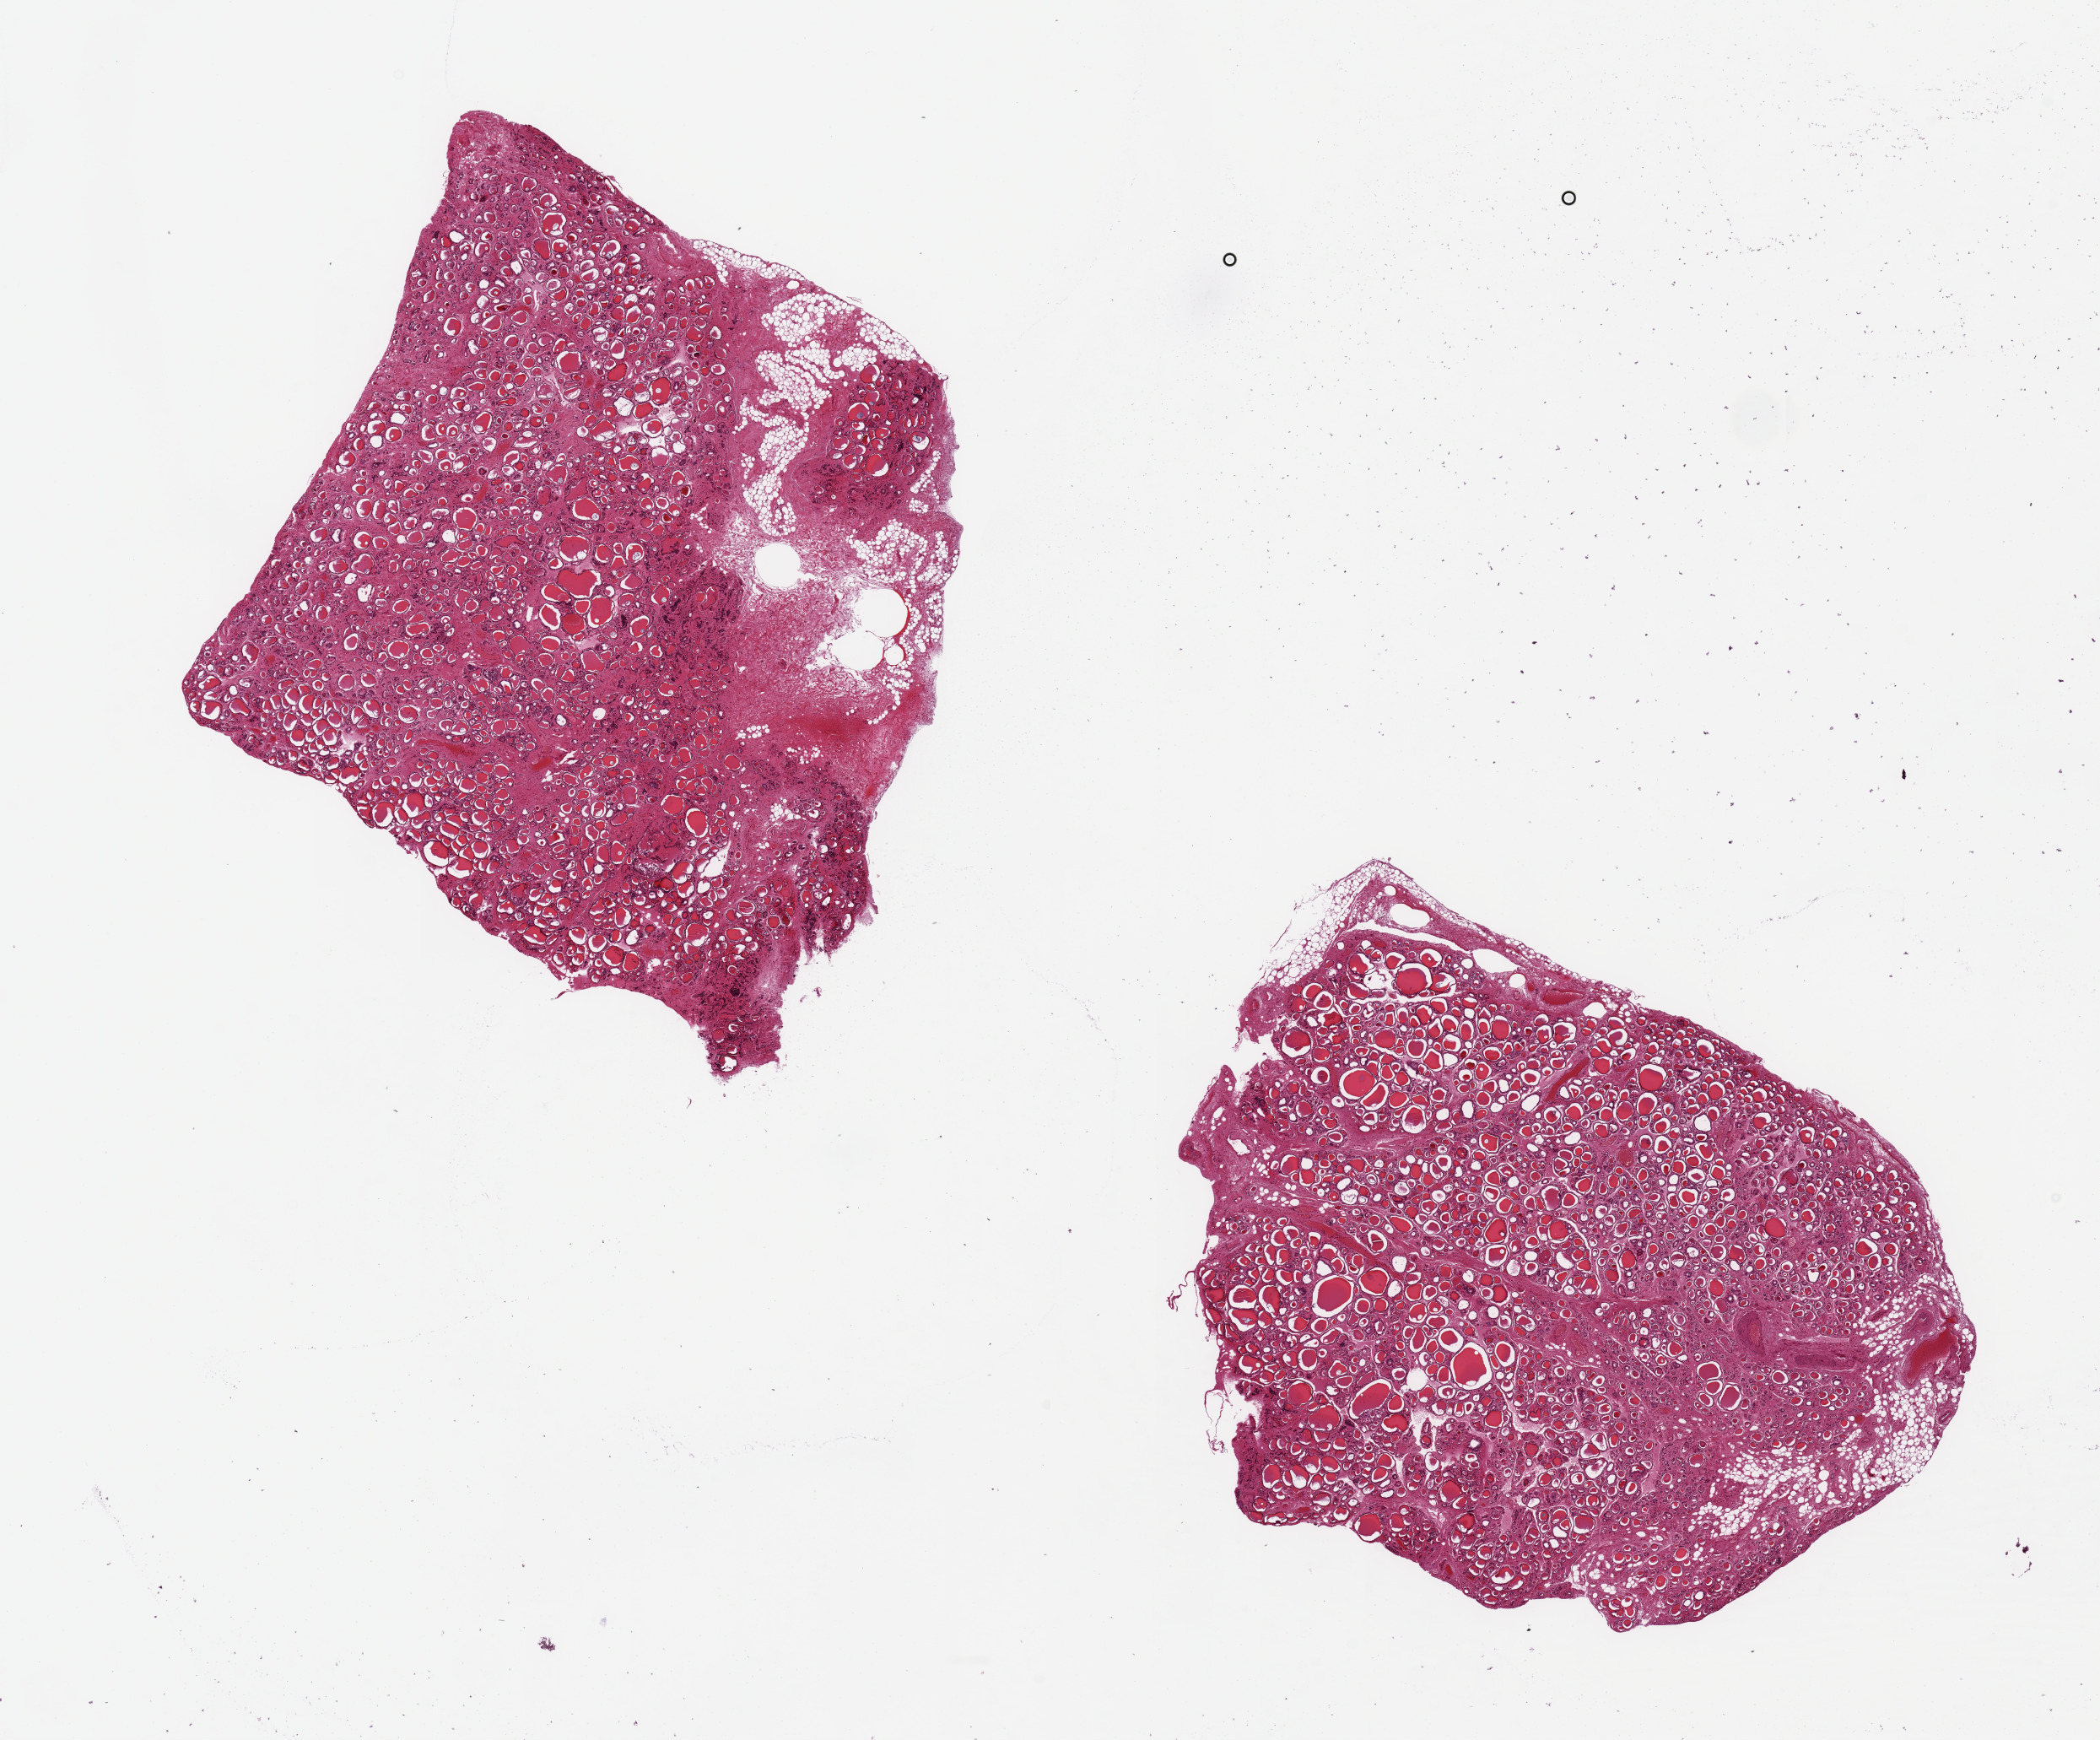
Digitized H&E-stained section, brightfield, whole scanned area (about 19.7 x 16.3 mm) shown as a low-resolution overview. PAXgene-fixed, paraffin-embedded tissue. Section of thyroid (target tissue). Tissue donor sample. Donor: male.
- reviewer comment on this tissue sample: 2 pieces, 6.5x6 & 7x6mm; interstitial fibrosis; ~10% adipose